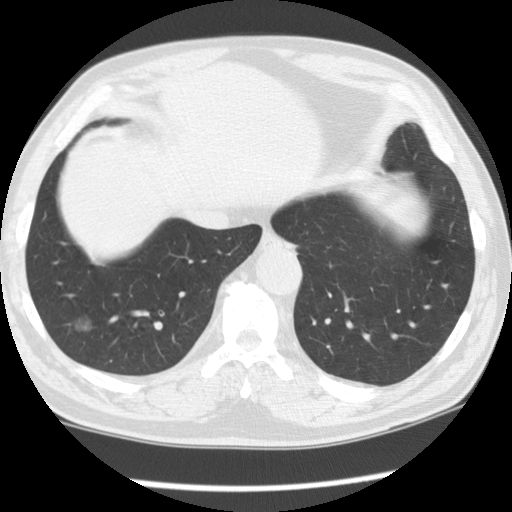
Low-dose screening chest CT, axial slice; first (baseline) screen; lung window (W 1500 / L -600 HU); 2.5 mm slice thickness; standard (soft-tissue) reconstruction kernel (STANDARD). Male participant, aged 62 years at enrolment.
Lesion marked by an expert reader, box from (x=51, y=300) to (x=113, y=361) px. Screening reader's record for this exam (one nodule recorded; not confirmed to be the boxed lesion): non-calcified nodule or mass ≥4 mm, right lower lobe, 13 × 11 mm, smooth margins, ground glass attenuation. Lung cancer was diagnosed 874 days after this screen: bronchiolo-alveolar carcinoma, non-mucinous, right lower lobe, well differentiated (G1), stage IA (AJCC 6th edition), 14 mm at pathology.